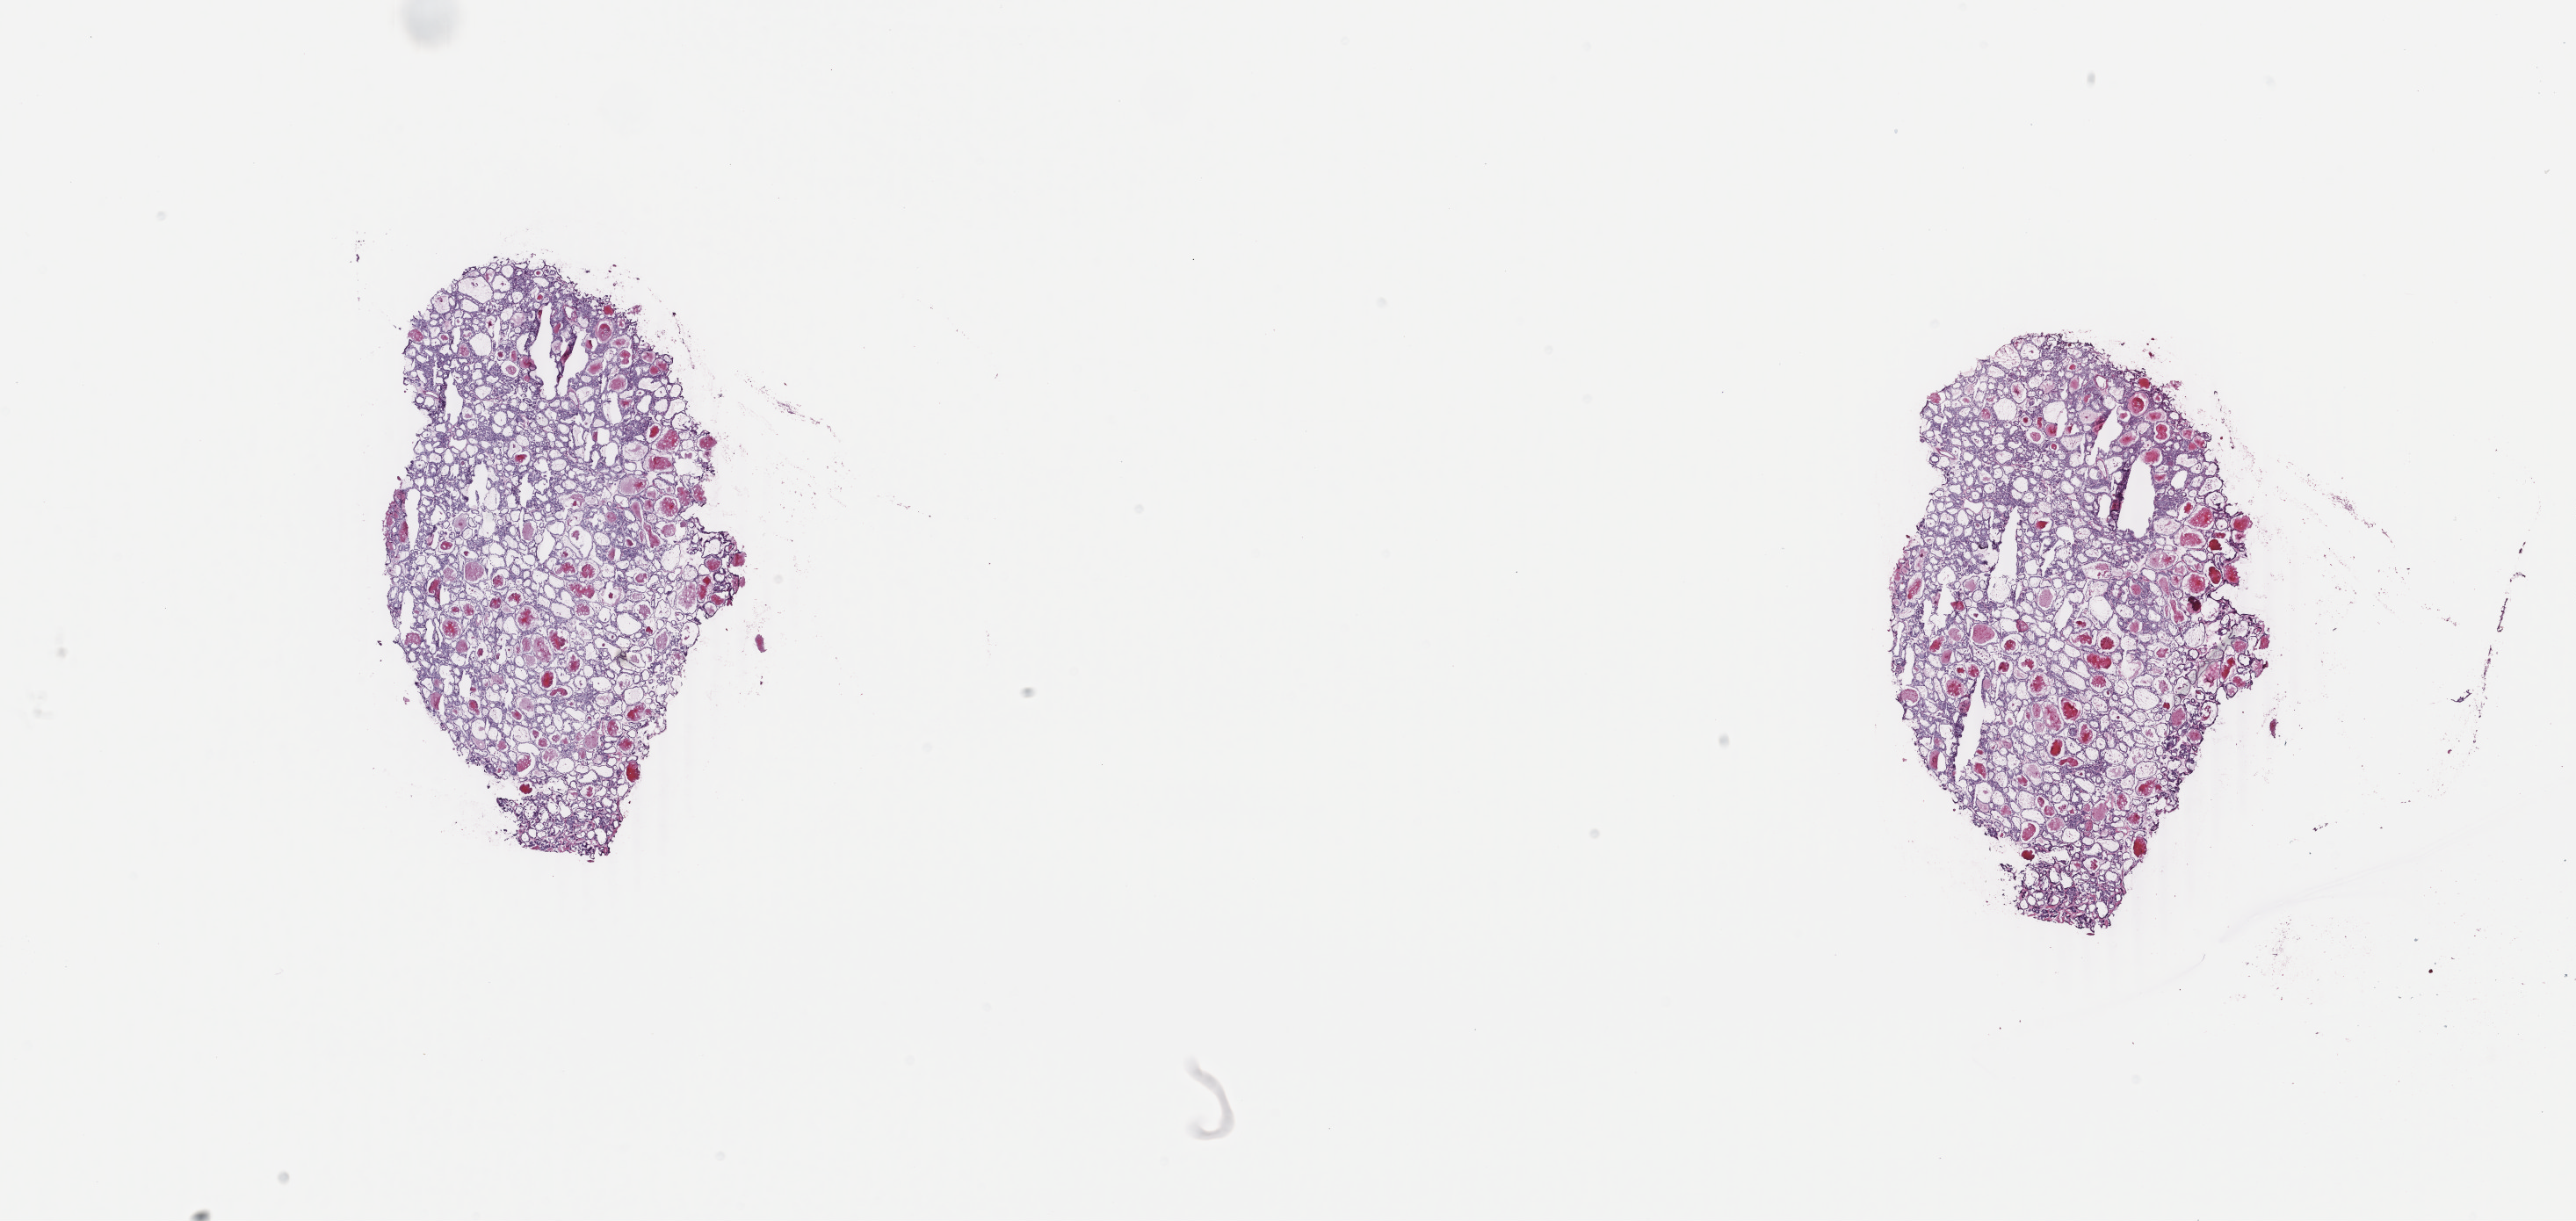
Whole-slide histology image, Hematoxylin and eosin (H&E) stained, whole scanned area (about 23.3 x 11.1 mm, from a 40x scan) shown as a low-resolution overview. Frozen section from the bottom of the tissue portion. Thyroid, primary tumour sample. Female, age 28 years at initial diagnosis. Composition of this section per pathologist review: tumour cells 100%, tumour nuclei 95%, normal cells 0%, stromal cells 0%, necrosis 0%. Infiltration values recorded for this section: lymphocyte infiltration 0%, monocyte infiltration 0%, neutrophil infiltration 0%.
• laterality: left
• histologic diagnosis: Papillary carcinoma, follicular variant (thyroid gland)
• AJCC pathologic stage: I (7th edition)